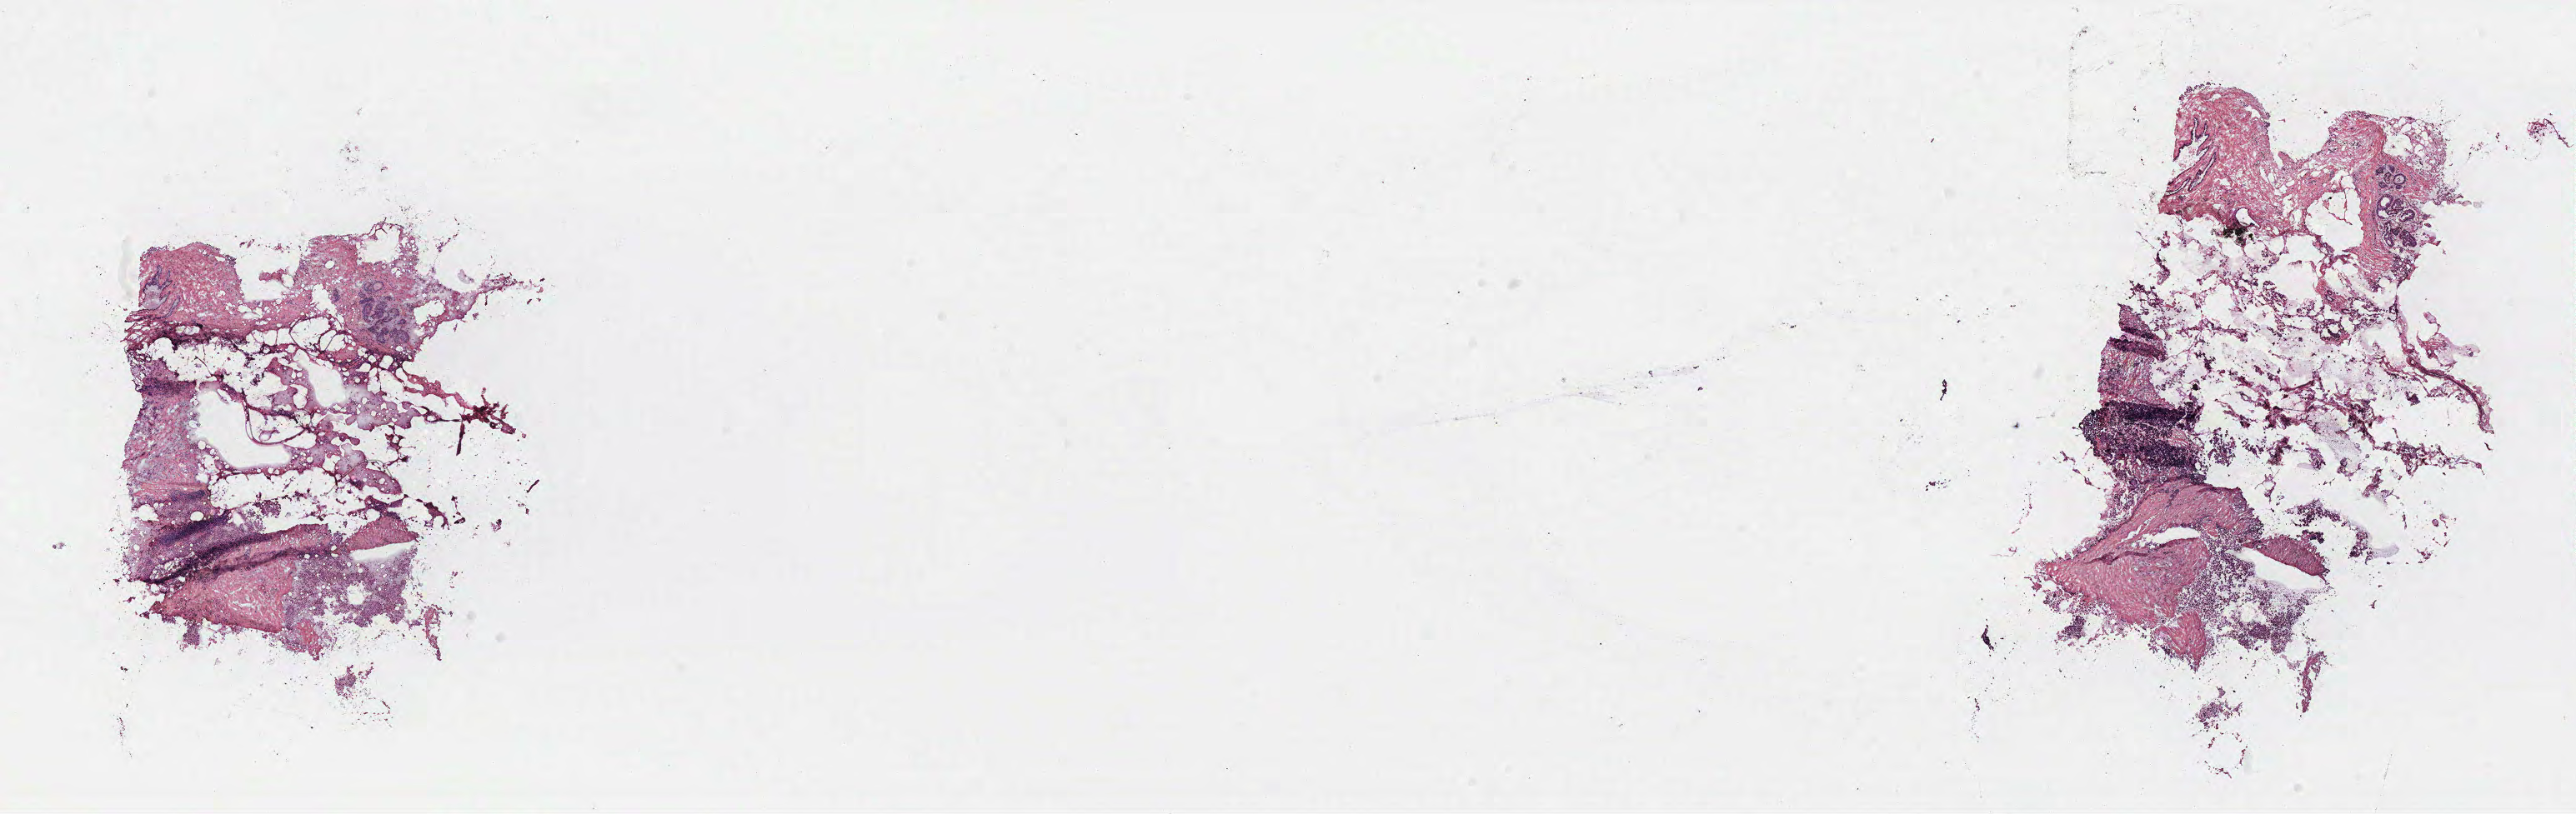
Digitized Hematoxylin and eosin (H&E) stained tissue section (whole slide), whole scanned area (about 24.7 x 7.8 mm) shown as a low-resolution overview; breast, tissue type not recorded.
Patient diagnosis (cohort enrolment): breast cancer (breast).